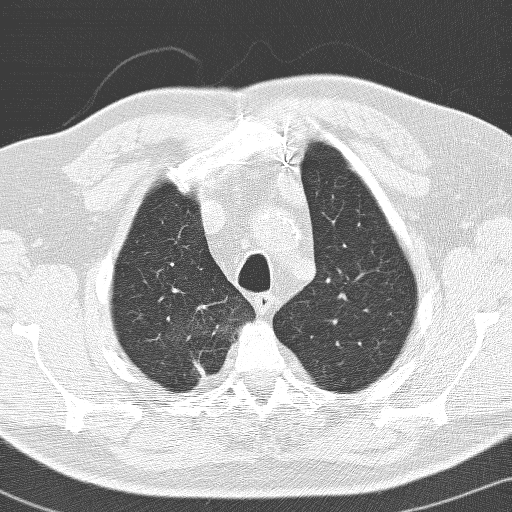
Low-dose screening chest CT, axial slice, baseline annual screen, lung window (W 1500 / L -600 HU), 3.2 mm slice thickness, slice 22 of 141 in the series, 512 × 512 image matrix, field of view 326 × 326 mm. Male participant, aged 66 years at enrolment.
Expert-annotated lung lesion, bounding box [x1, y1, x2, y2] px = [156, 322, 231, 395]. Screening reader's record for this exam (one nodule recorded; not confirmed to be the boxed lesion): non-calcified nodule or mass ≥4 mm, right upper lobe, 36 × 30 mm, spiculated (stellate) margins, soft tissue attenuation. Participant outcome: lung cancer diagnosed 103 days after this screen — adenocarcinoma, NOS, right upper lobe, poorly differentiated (G3), stage IIB (AJCC 6th edition), 33 mm at pathology.